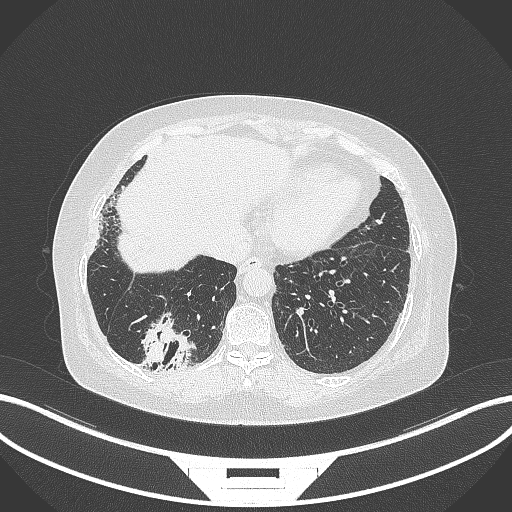
Chest CT, one axial slice. Position 48 of 296 along the scan axis. 120 kVp. Lung window (W 1500 / L -600 HU). 1 mm slice thickness. 512 × 512 image matrix, field of view 400 × 400 mm. Patient: female, 65 years. From the clinical record (not read from this slice): clinical TNM (as recorded): T2b N1 M0.
Annotated regions visible in this slice (rectangle marked by the reading radiologist):
- lung tumour (recorded histology: adenocarcinoma): bounding box [x1, y1, x2, y2] px = [136, 312, 196, 374]